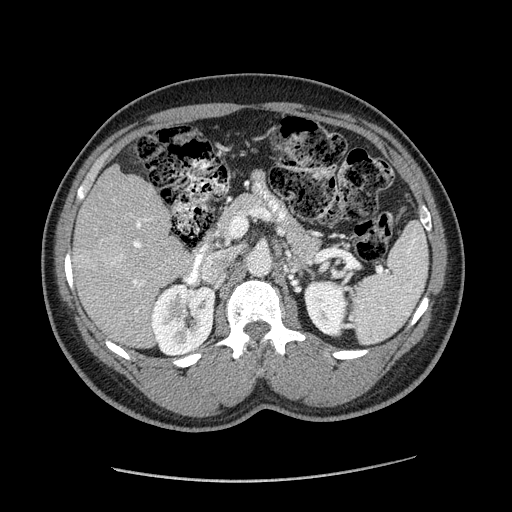
Contrast-enhanced abdominal CT (liver protocol), one axial slice; slice 87 of 182 in the series (ordered by position); reconstruction kernel STANDARD; 120 kVp; soft-tissue window (W 400 / L 40 HU); 512 × 512 image matrix. From the clinical record (not read from this slice): diagnosis: hepatocellular carcinoma (patient treated with transarterial chemoembolisation; whether this scan precedes or follows treatment is not stated here); TNM stage (as recorded): Stage-I; Child-Pugh class: A; tumour nodularity: uninodular.
Annotated regions visible in this slice (semi-automatic segmentation, software-assisted and operator-edited):
- liver parenchyma outside the tumour (the mass and vessels are separate outlines, so this box may not span the whole liver): bounding box (x1, y1, x2, y2) in pixels: (72, 166, 192, 348)
- mass: (91, 228, 130, 266)
- liver vessels: (133, 219, 148, 313)